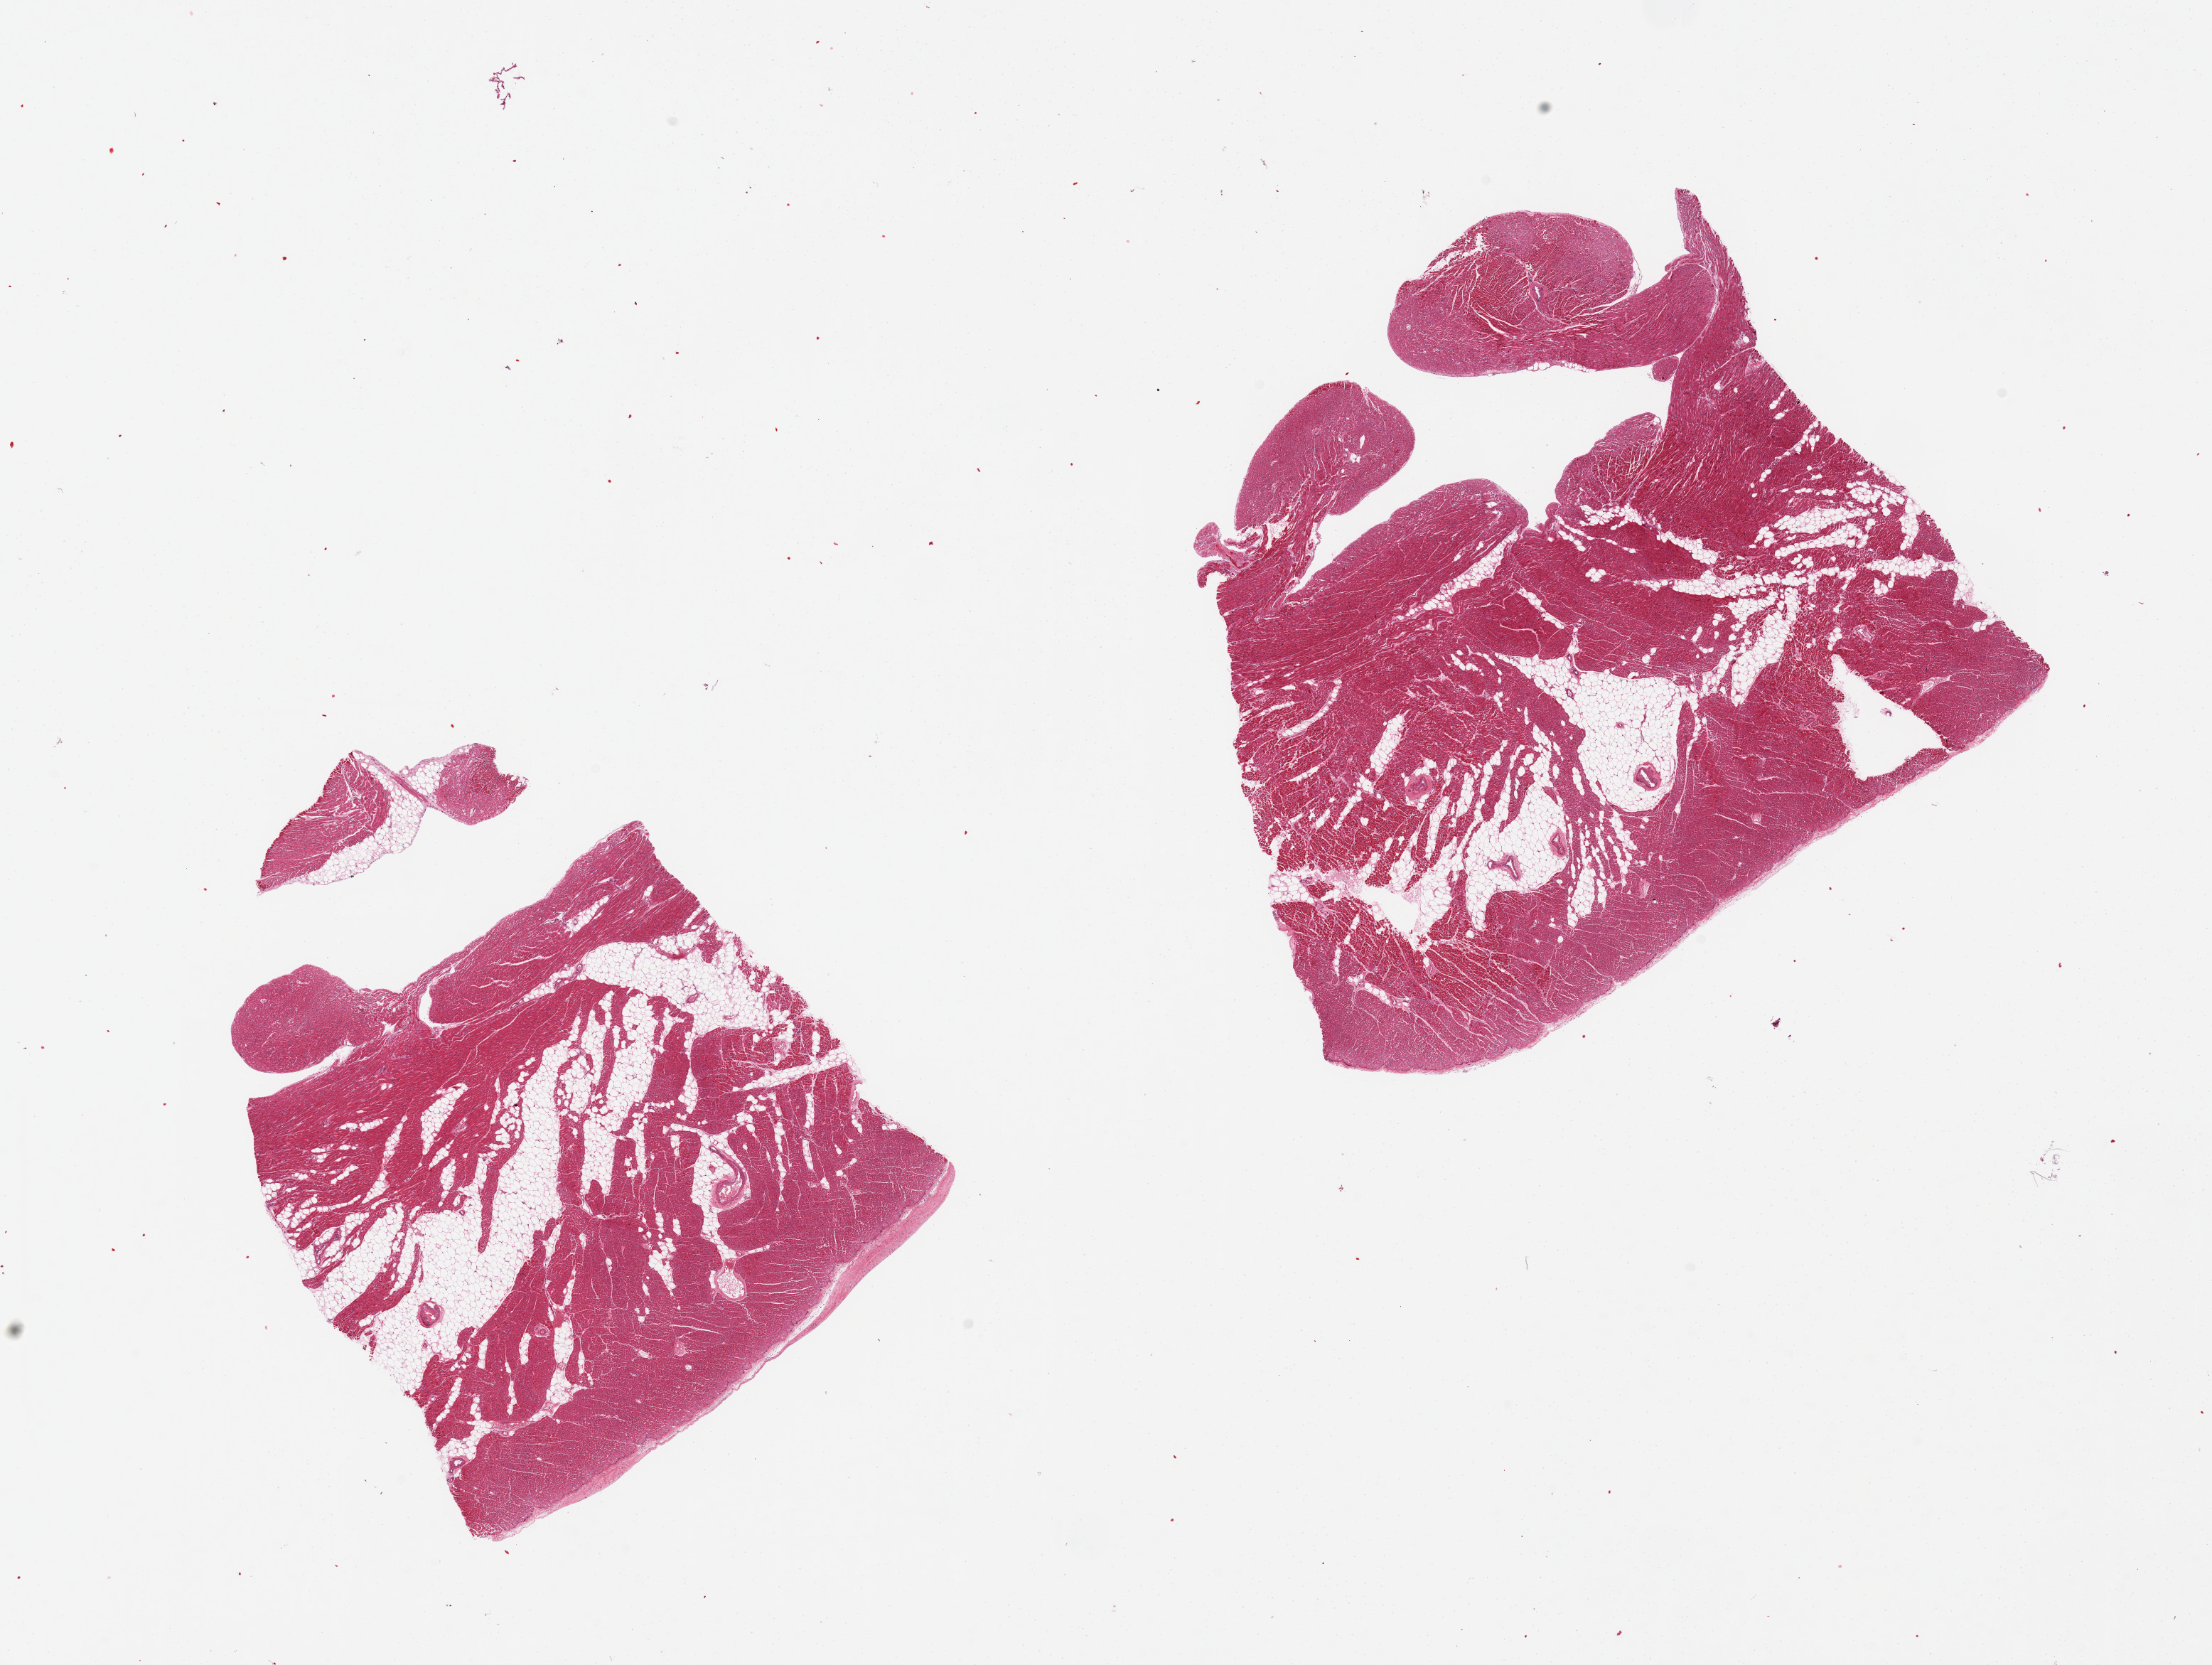
Whole-slide image, H&E stain, brightfield — low-resolution overview of the scanned area, about 24.6 x 18.5 mm; PAXgene-fixed paraffin-embedded (PFPE) section; section of heart (target tissue); tissue donor sample. Female donor.
Reviewer comment on this tissue sample: 2 pieces, 10-20% internal fat.